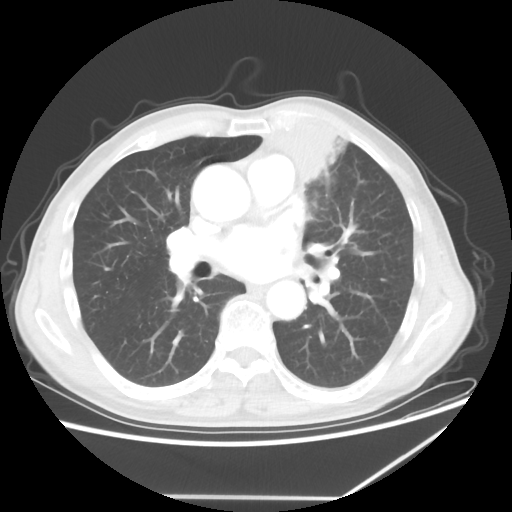
Chest CT, one axial slice; position 33 of 64 along the scan axis; reconstruction kernel STANDARD; 100 kVp; lung window (W 1500 / L -600 HU); 5 mm slice thickness; 512 × 512 image matrix. Patient: male, 64 years. From the clinical record (not read from this slice): clinical TNM (as recorded): T1c N1 M1; histopathological grade: G2.
Outlined on this slice (rectangle marked by the reading radiologist):
- lung tumour (recorded histology: squamous cell carcinoma): bounding box (x1, y1, x2, y2) in pixels: (253, 112, 345, 175)